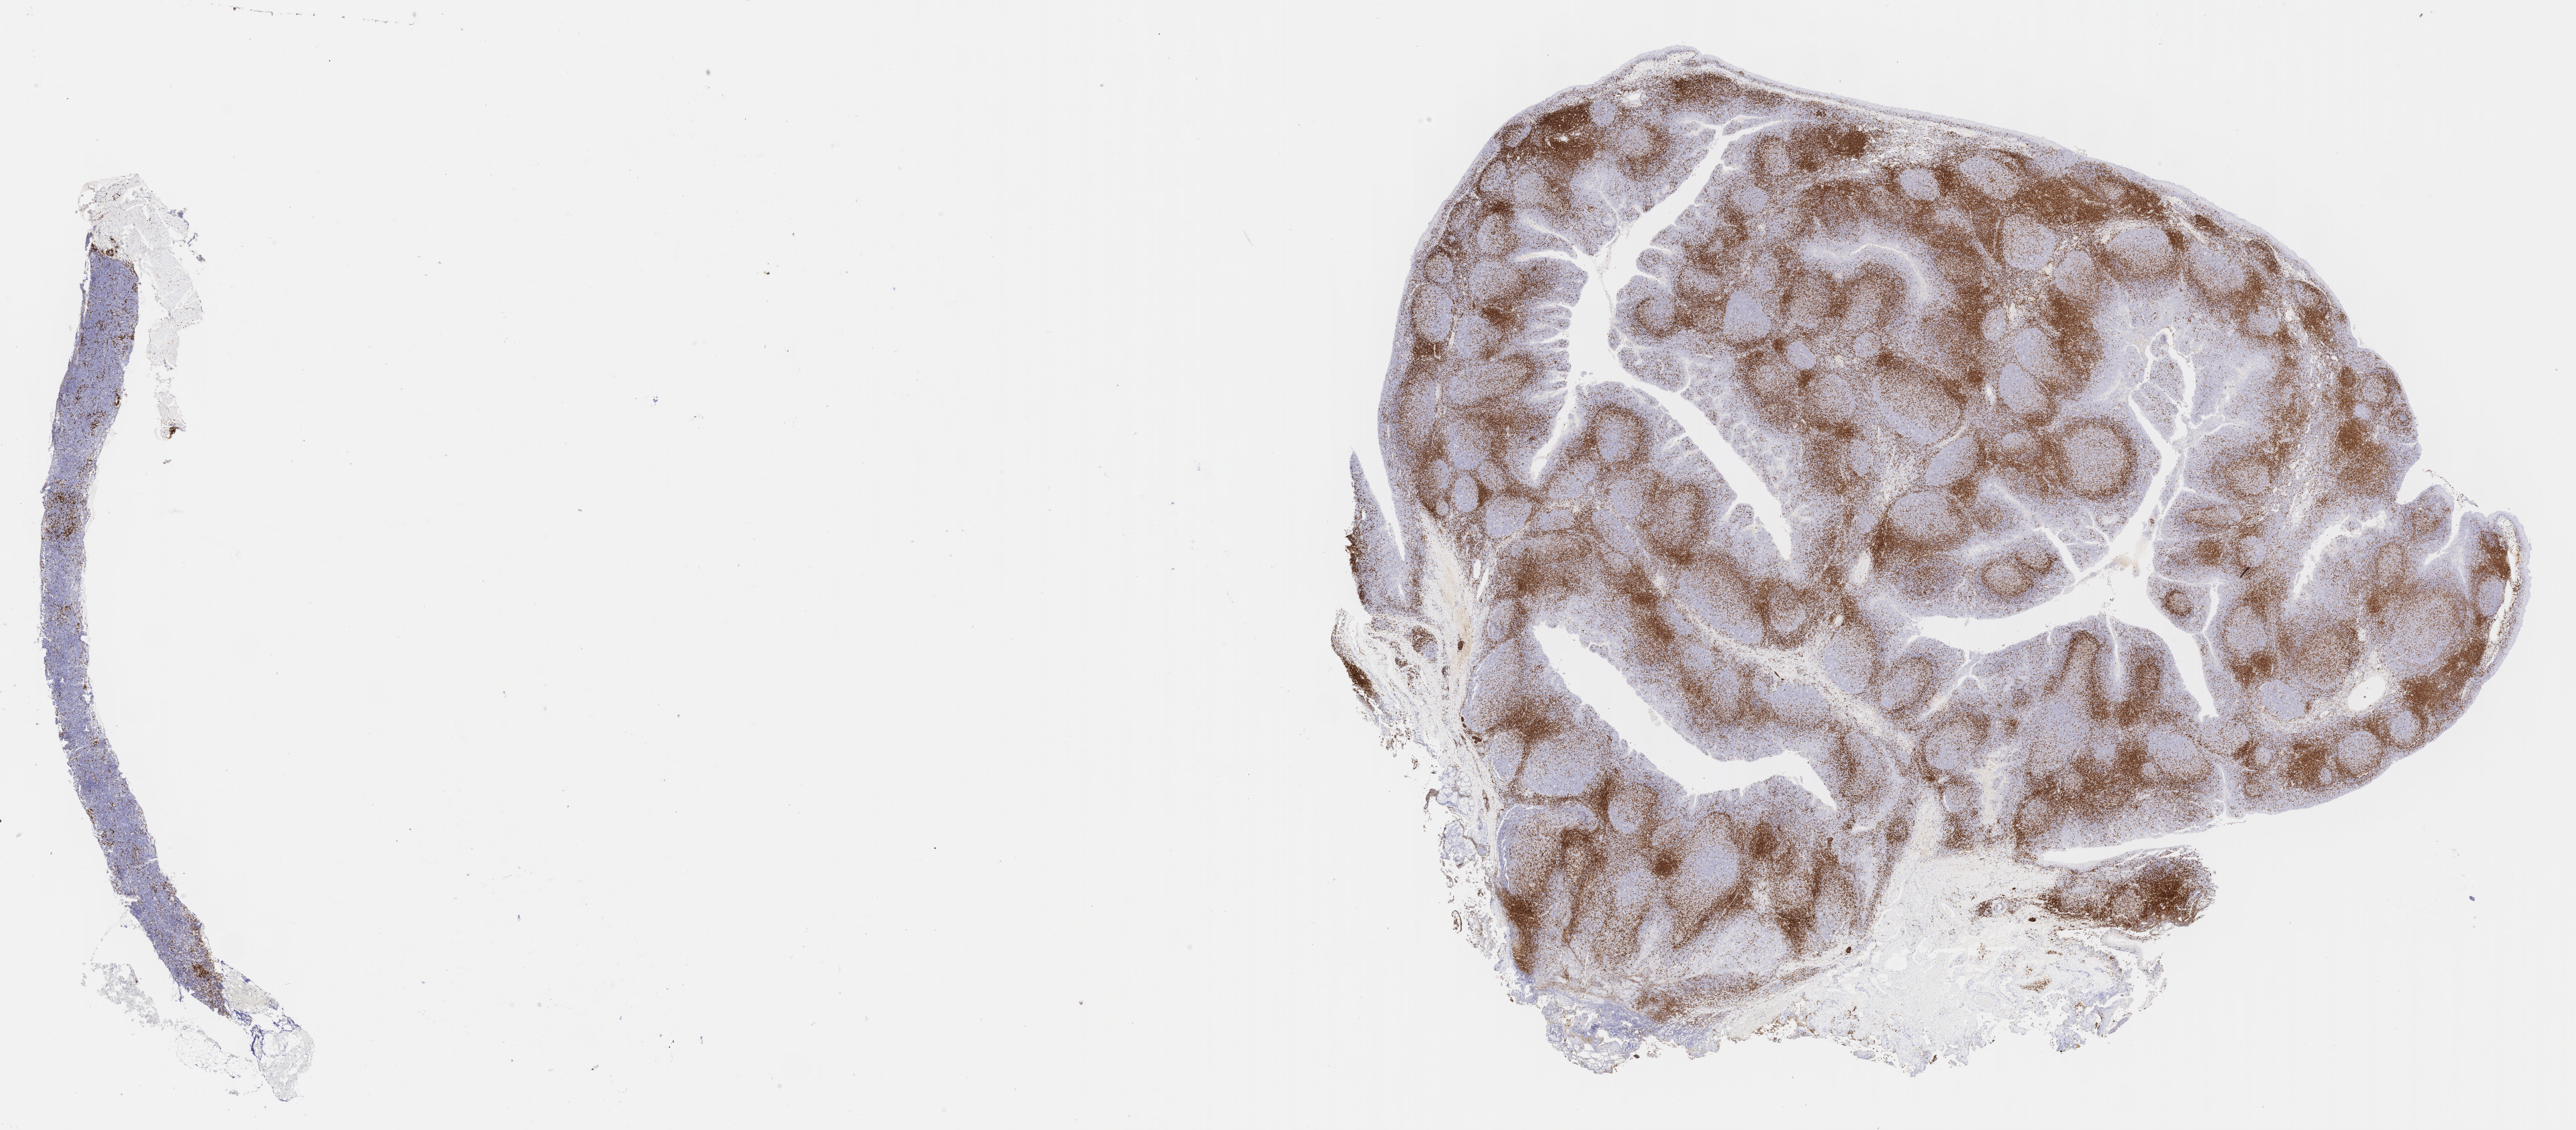
Whole-slide image, immunohistochemical stain for CD3, whole scanned area (about 31.2 x 13.7 mm) shown as a low-resolution overview, tumor tissue, site: cranium. Patient: female, age at initial diagnosis 7 years.
Diagnosis: Burkitt lymphoma, NOS.